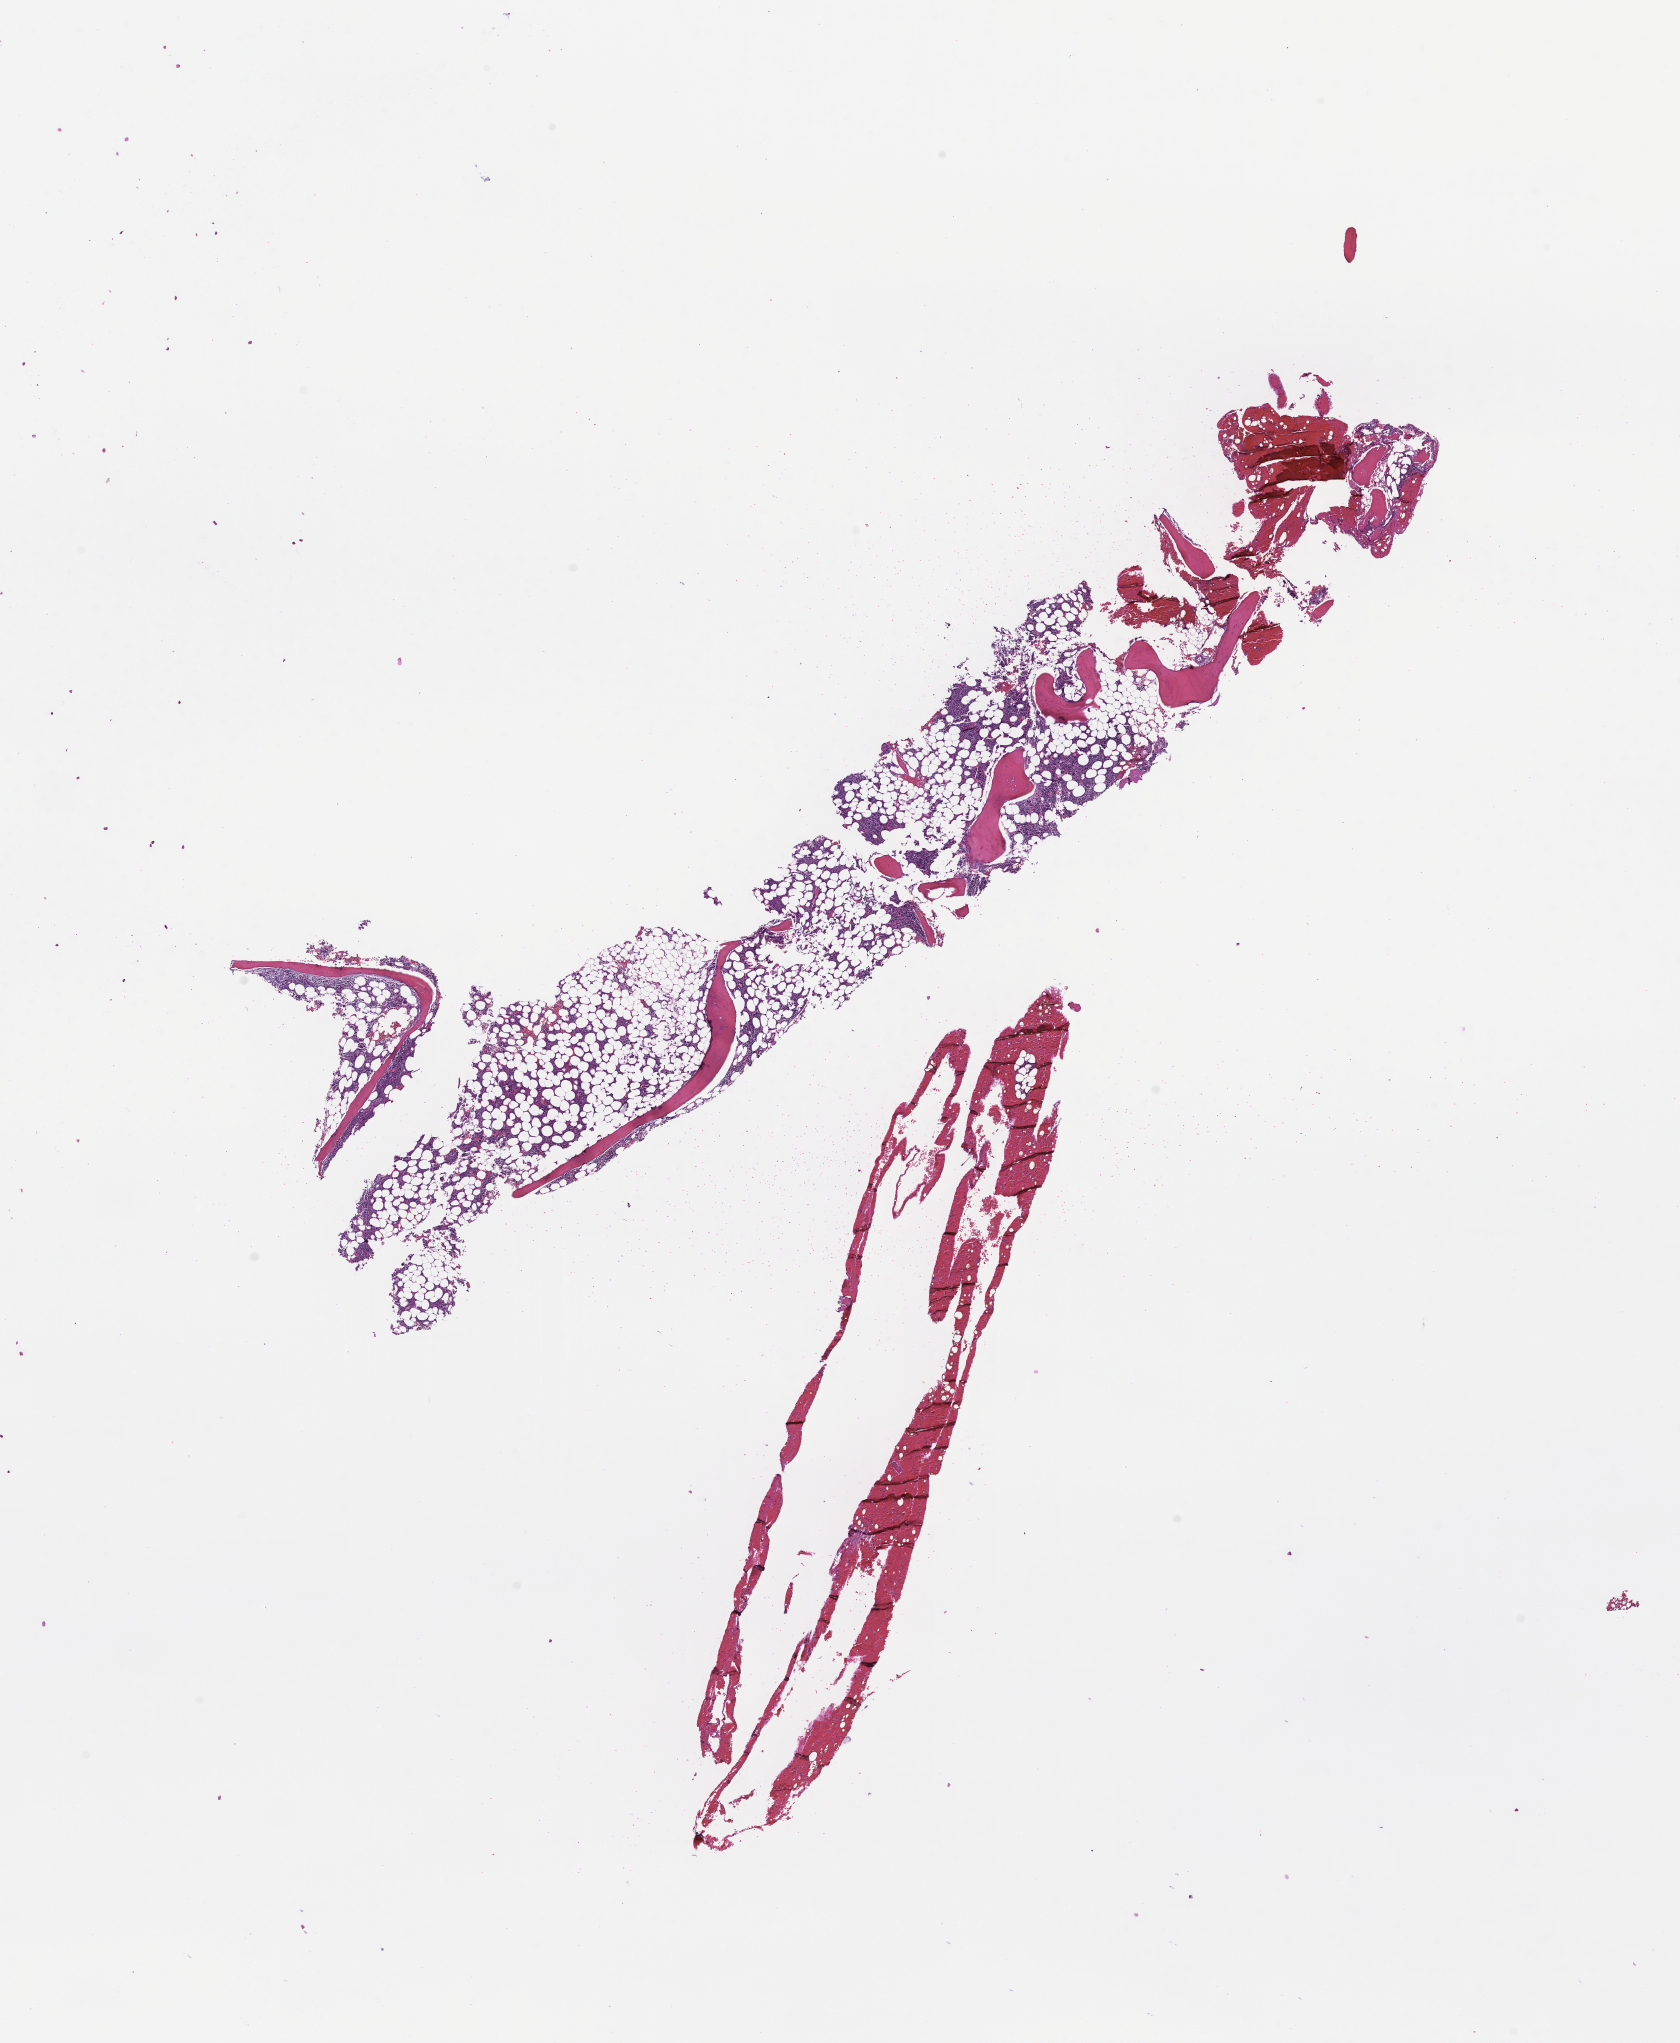
H&E whole-slide image — whole scanned area (about 13.6 x 16.5 mm) shown as a low-resolution overview. FFPE section. Tissue site: bone marrow. Patient: male.
This section: primary tumour tissue. Diagnosis: Plasma Cell Myeloma.